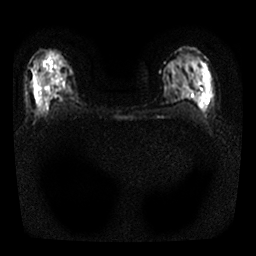
Breast MRI, one axial slice; position 15 of 25 along the scan axis; diffusion-weighted series; image 2 of 4 stored at this slice position (different b-values; order by instance number); 1.5 T; 256 × 256 image matrix, field of view 300 × 300 mm. Female patient.
Outlined on this slice (outlined manually by an expert reader):
- tumour on diffusion-weighted imaging: bounding box (x1, y1, x2, y2) in pixels: (35, 60, 52, 110)